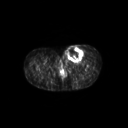
FDG PET of an extremity soft-tissue mass (from a PET/CT study), one axial slice. Position 53 of 267 along the scan axis. 3.27 mm slice thickness. 128 × 128 image matrix, field of view 600 × 600 mm. Female patient, age 24 years. Case-level facts recorded for this patient, not image findings: histological type: leiomyosarcoma; grade: high; site of the primary tumour: groin.
Outlined on this slice (expert contour drawn on MRI and transferred to this co-registered scan by the dataset authors):
- gross tumour volume including surrounding oedema: box from (x=63, y=44) to (x=87, y=61) px
- gross tumour volume (mass): (x=66, y=45)–(x=84, y=61)